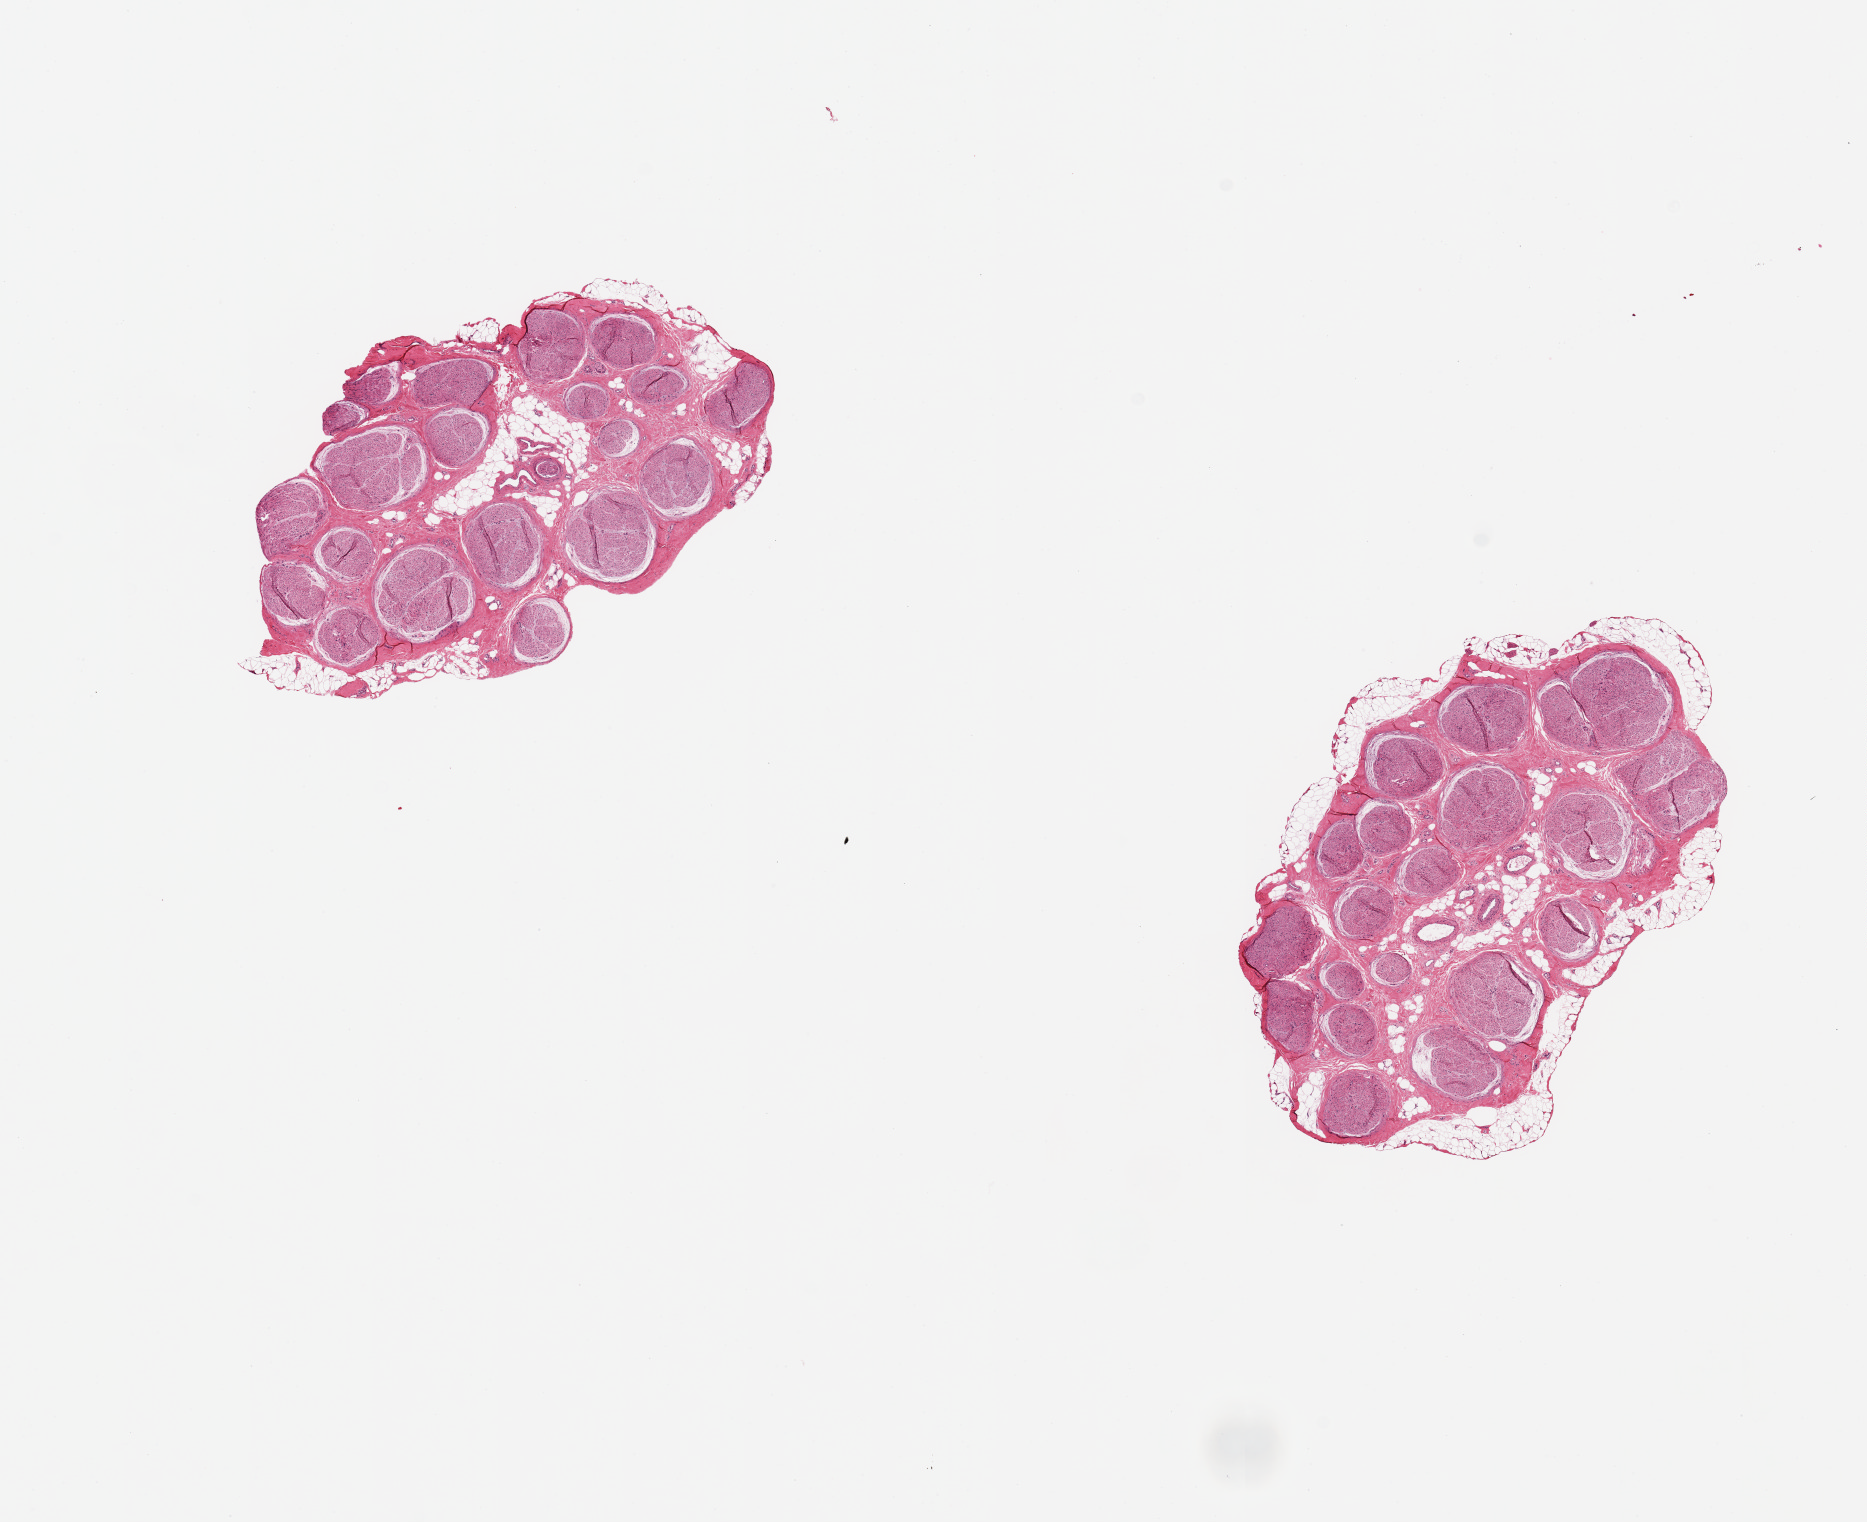
Whole-slide image, haematoxylin and eosin stain — low-resolution overview of the scanned area, about 14.8 x 12.0 mm (from a 20x scan). PAXgene-fixed, paraffin-embedded tissue. Section of tibial nerve (target tissue). Tissue donor sample.
Pathologist's review note for this sample: 2 pieces, 5x3 & 5x3mm; up to 0.3mm adipose around each piece.